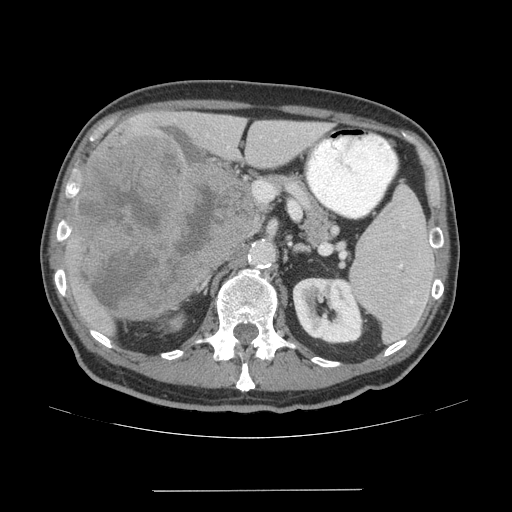
Contrast-enhanced abdominal CT (liver protocol), one axial slice. Slice 28 of 77 in the series (ordered by position). Reconstruction kernel STANDARD. Soft-tissue window (W 400 / L 40 HU). 2.5 mm slice thickness. 512 × 512 image matrix, field of view 400 × 400 mm. Case-level facts recorded for this patient, not image findings: diagnosis: hepatocellular carcinoma (patient treated with transarterial chemoembolisation; whether this scan precedes or follows treatment is not stated here); TNM stage (as recorded): Stage-IVA; Child-Pugh class: A.
Structures marked on this image (semi-automatically segmented with operator editing):
- liver parenchyma outside the tumour (the mass and vessels are separate outlines, so this box may not span the whole liver): bounding box <64,112,325,332> (left, top, right, bottom; pixels)
- mass: <72,139,255,320>